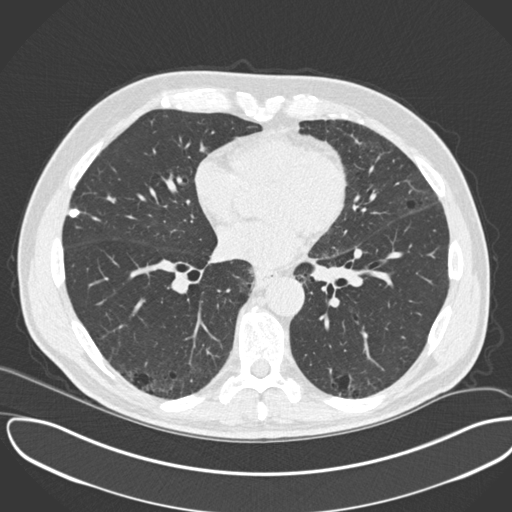
Low-dose screening chest CT, one axial slice. Position 110 of 245 along the scan axis. Reconstruction kernel B30f. 120 kVp. Lung window (W 1500 / L -600 HU). 2 mm slice thickness. 512 × 512 image matrix, field of view 396 × 396 mm.
Annotated regions visible in this slice (manually delineated by an expert):
- lesion 1 (tumor, upper lobe of right lung): box from (x=70, y=209) to (x=80, y=218) px